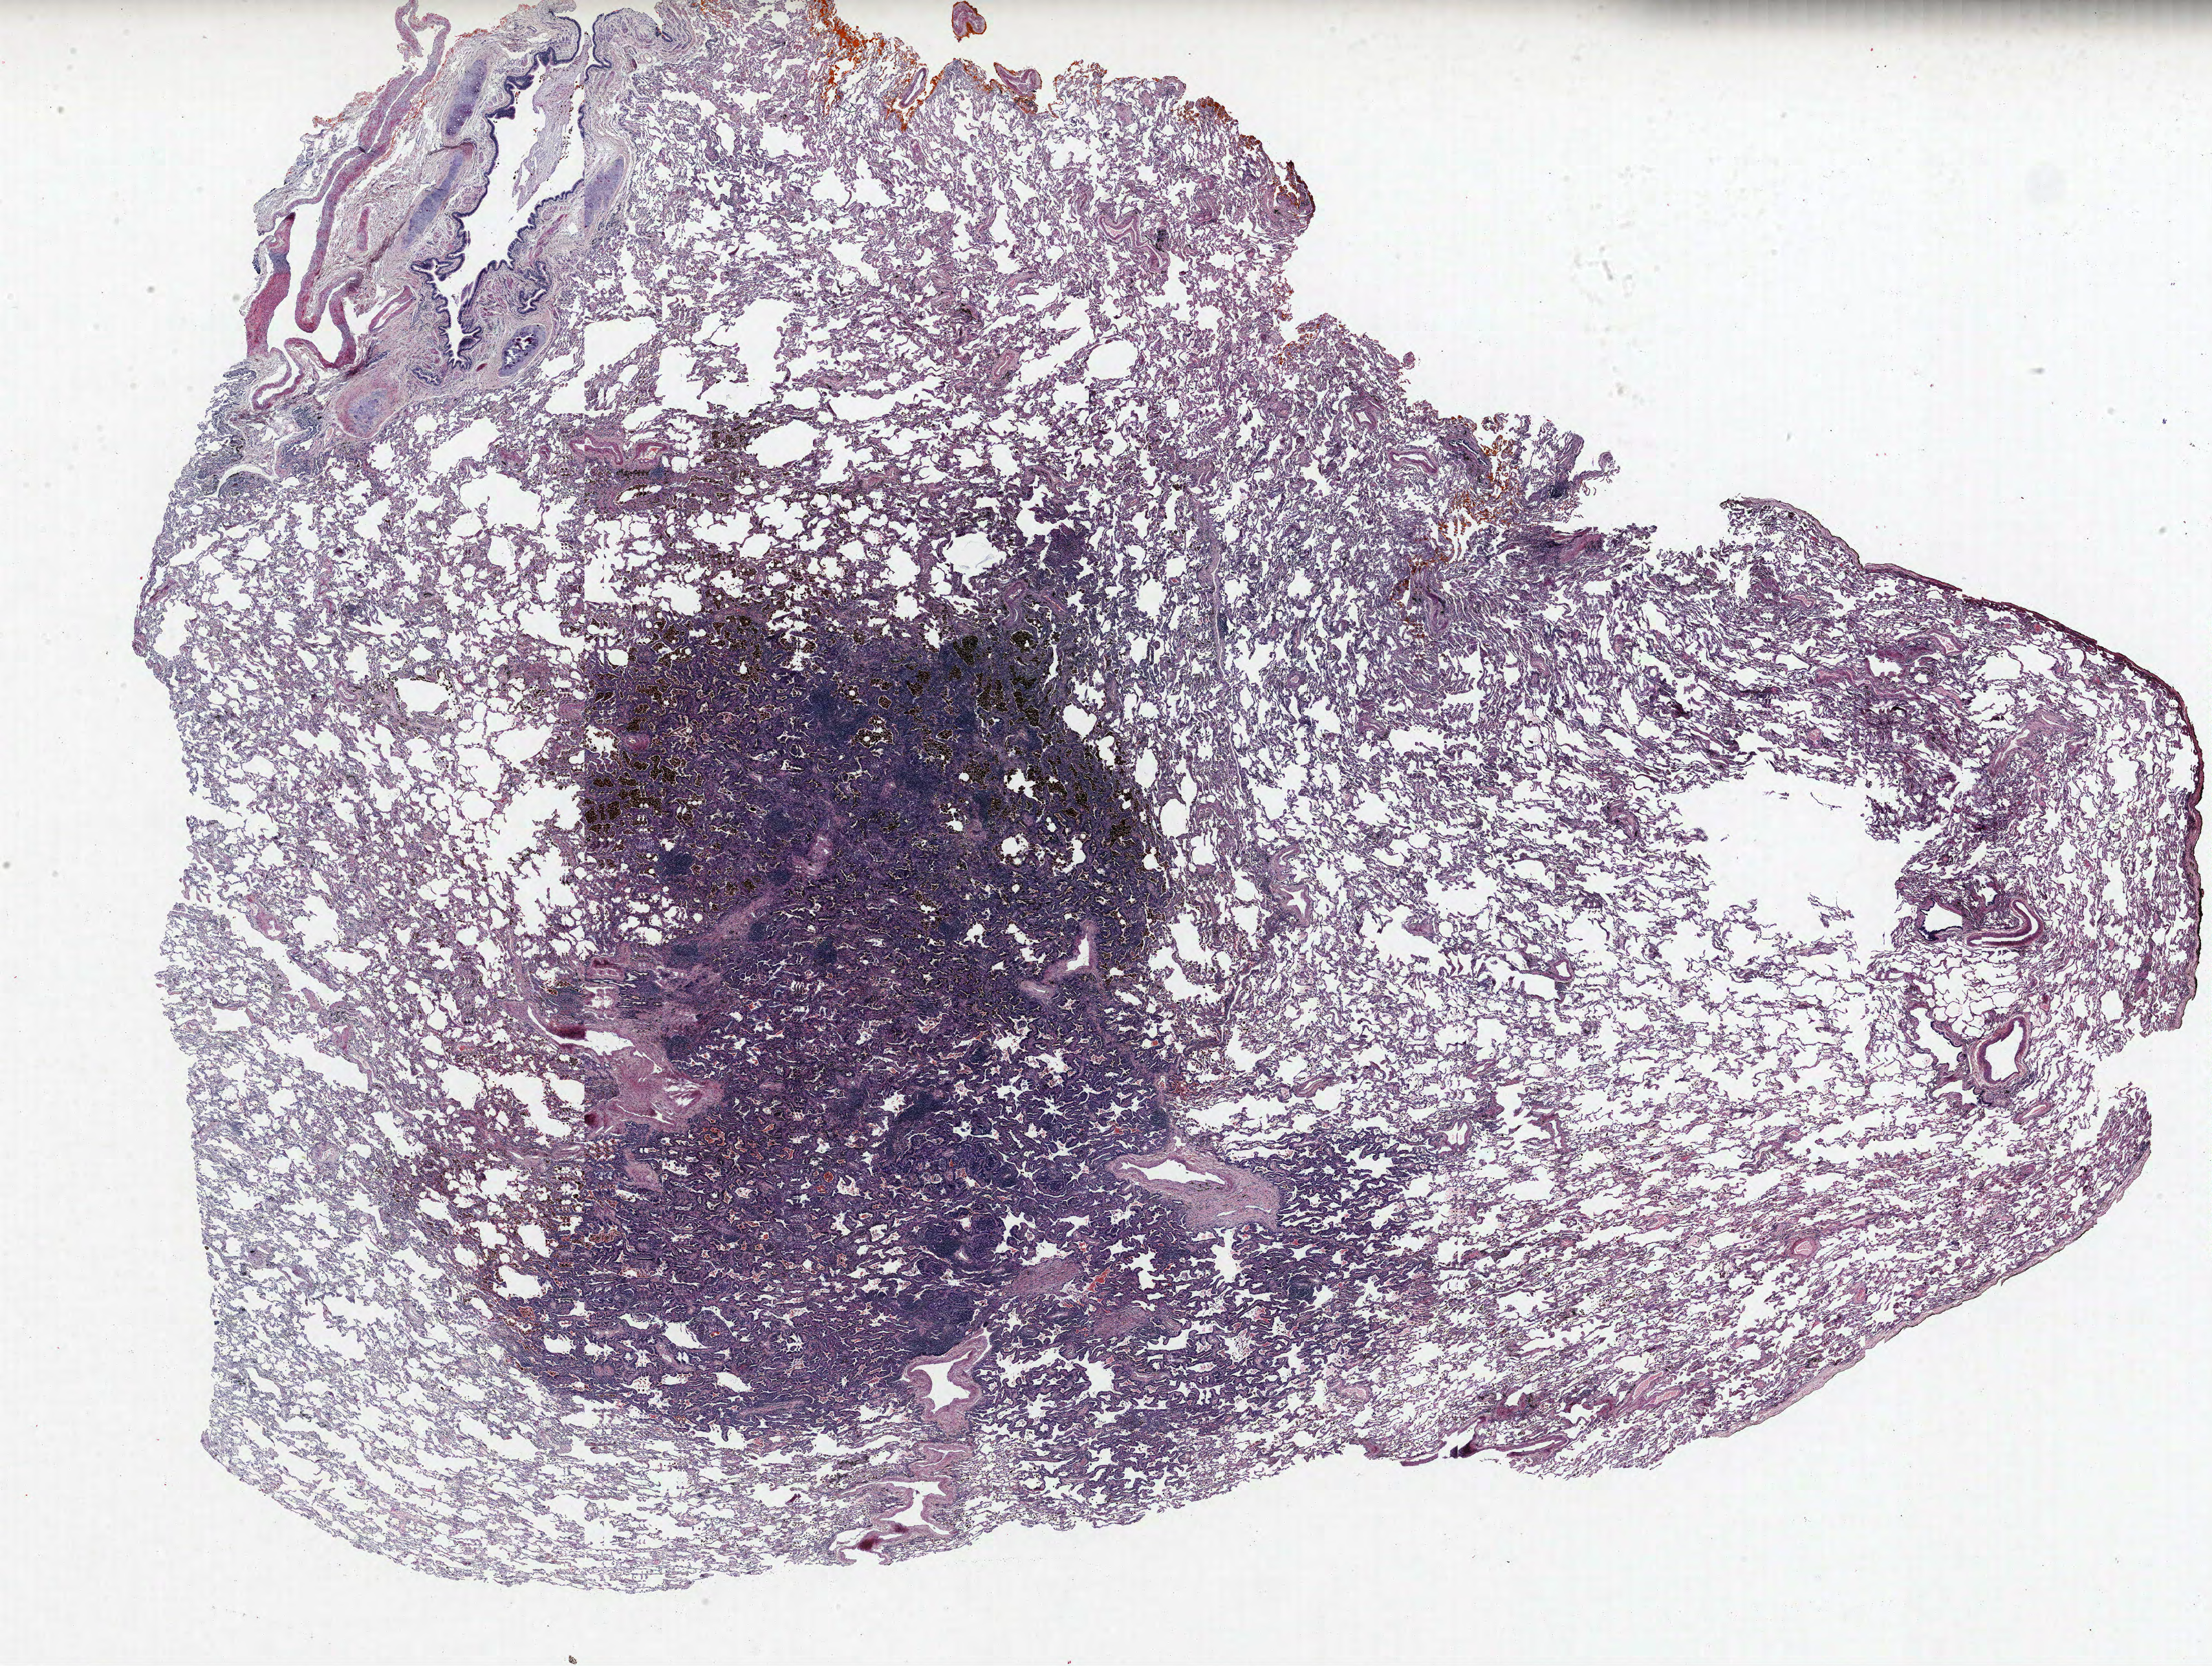
H&E whole-slide image, whole scanned area (about 27.4 x 20.6 mm) shown as a low-resolution overview. Formalin-fixed paraffin-embedded (FFPE) section. Lung tissue. Male patient, aged 60 at enrolment. Former smoker at enrolment. Grade: well differentiated (G1).
Primary tumour location (clinical record): left upper lobe. Tumour size (pathology): 16 mm. Participant's lung-cancer diagnosis: Bronchiolo-alveolar carcinoma, non-mucinous (ICD-O-3 8252/3). Stage (AJCC 6th edition): IA.